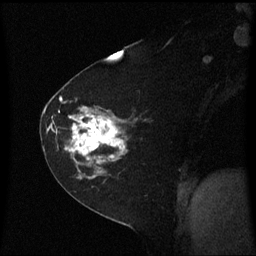
Breast MRI (dynamic contrast-enhanced), one sagittal slice. Slice 39 of 60 in the series (ordered by position). Dynamic contrast-enhanced series, image 2 of 3 at this slice position (ordered by acquisition). 1.5 T. TE 4.2 ms, TR 8.4 ms. 256 × 256 image matrix, field of view 210 × 210 mm. Patient: female, 60 years. Case-level facts recorded for this patient, not image findings: setting: breast cancer imaged before/during neoadjuvant chemotherapy; receptor status: triple-negative.
Structures marked on this image (semi-automatic segmentation, software-assisted and operator-edited):
- analysis volume of interest (the breast-tissue region the enhancement analysis was run in; not a lesion): box from (x=45, y=99) to (x=149, y=182) px
- tumour enhancement mask (voxels above the 70 % enhancement threshold inside the analysis volume of interest): (x=46, y=99)–(x=128, y=164)